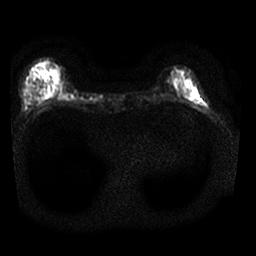
Breast MRI, one axial slice; slice 6 of 25 in the series (ordered by position); diffusion-weighted series; image 2 of 4 stored at this slice position (different b-values; order by instance number); 1.5 T; 4 mm slice thickness; 256 × 256 image matrix, field of view 310 × 310 mm. Female patient.
Annotated regions visible in this slice (outlined manually by an expert reader):
- tumour on diffusion-weighted imaging: bounding box <54,76,59,81> (left, top, right, bottom; pixels)